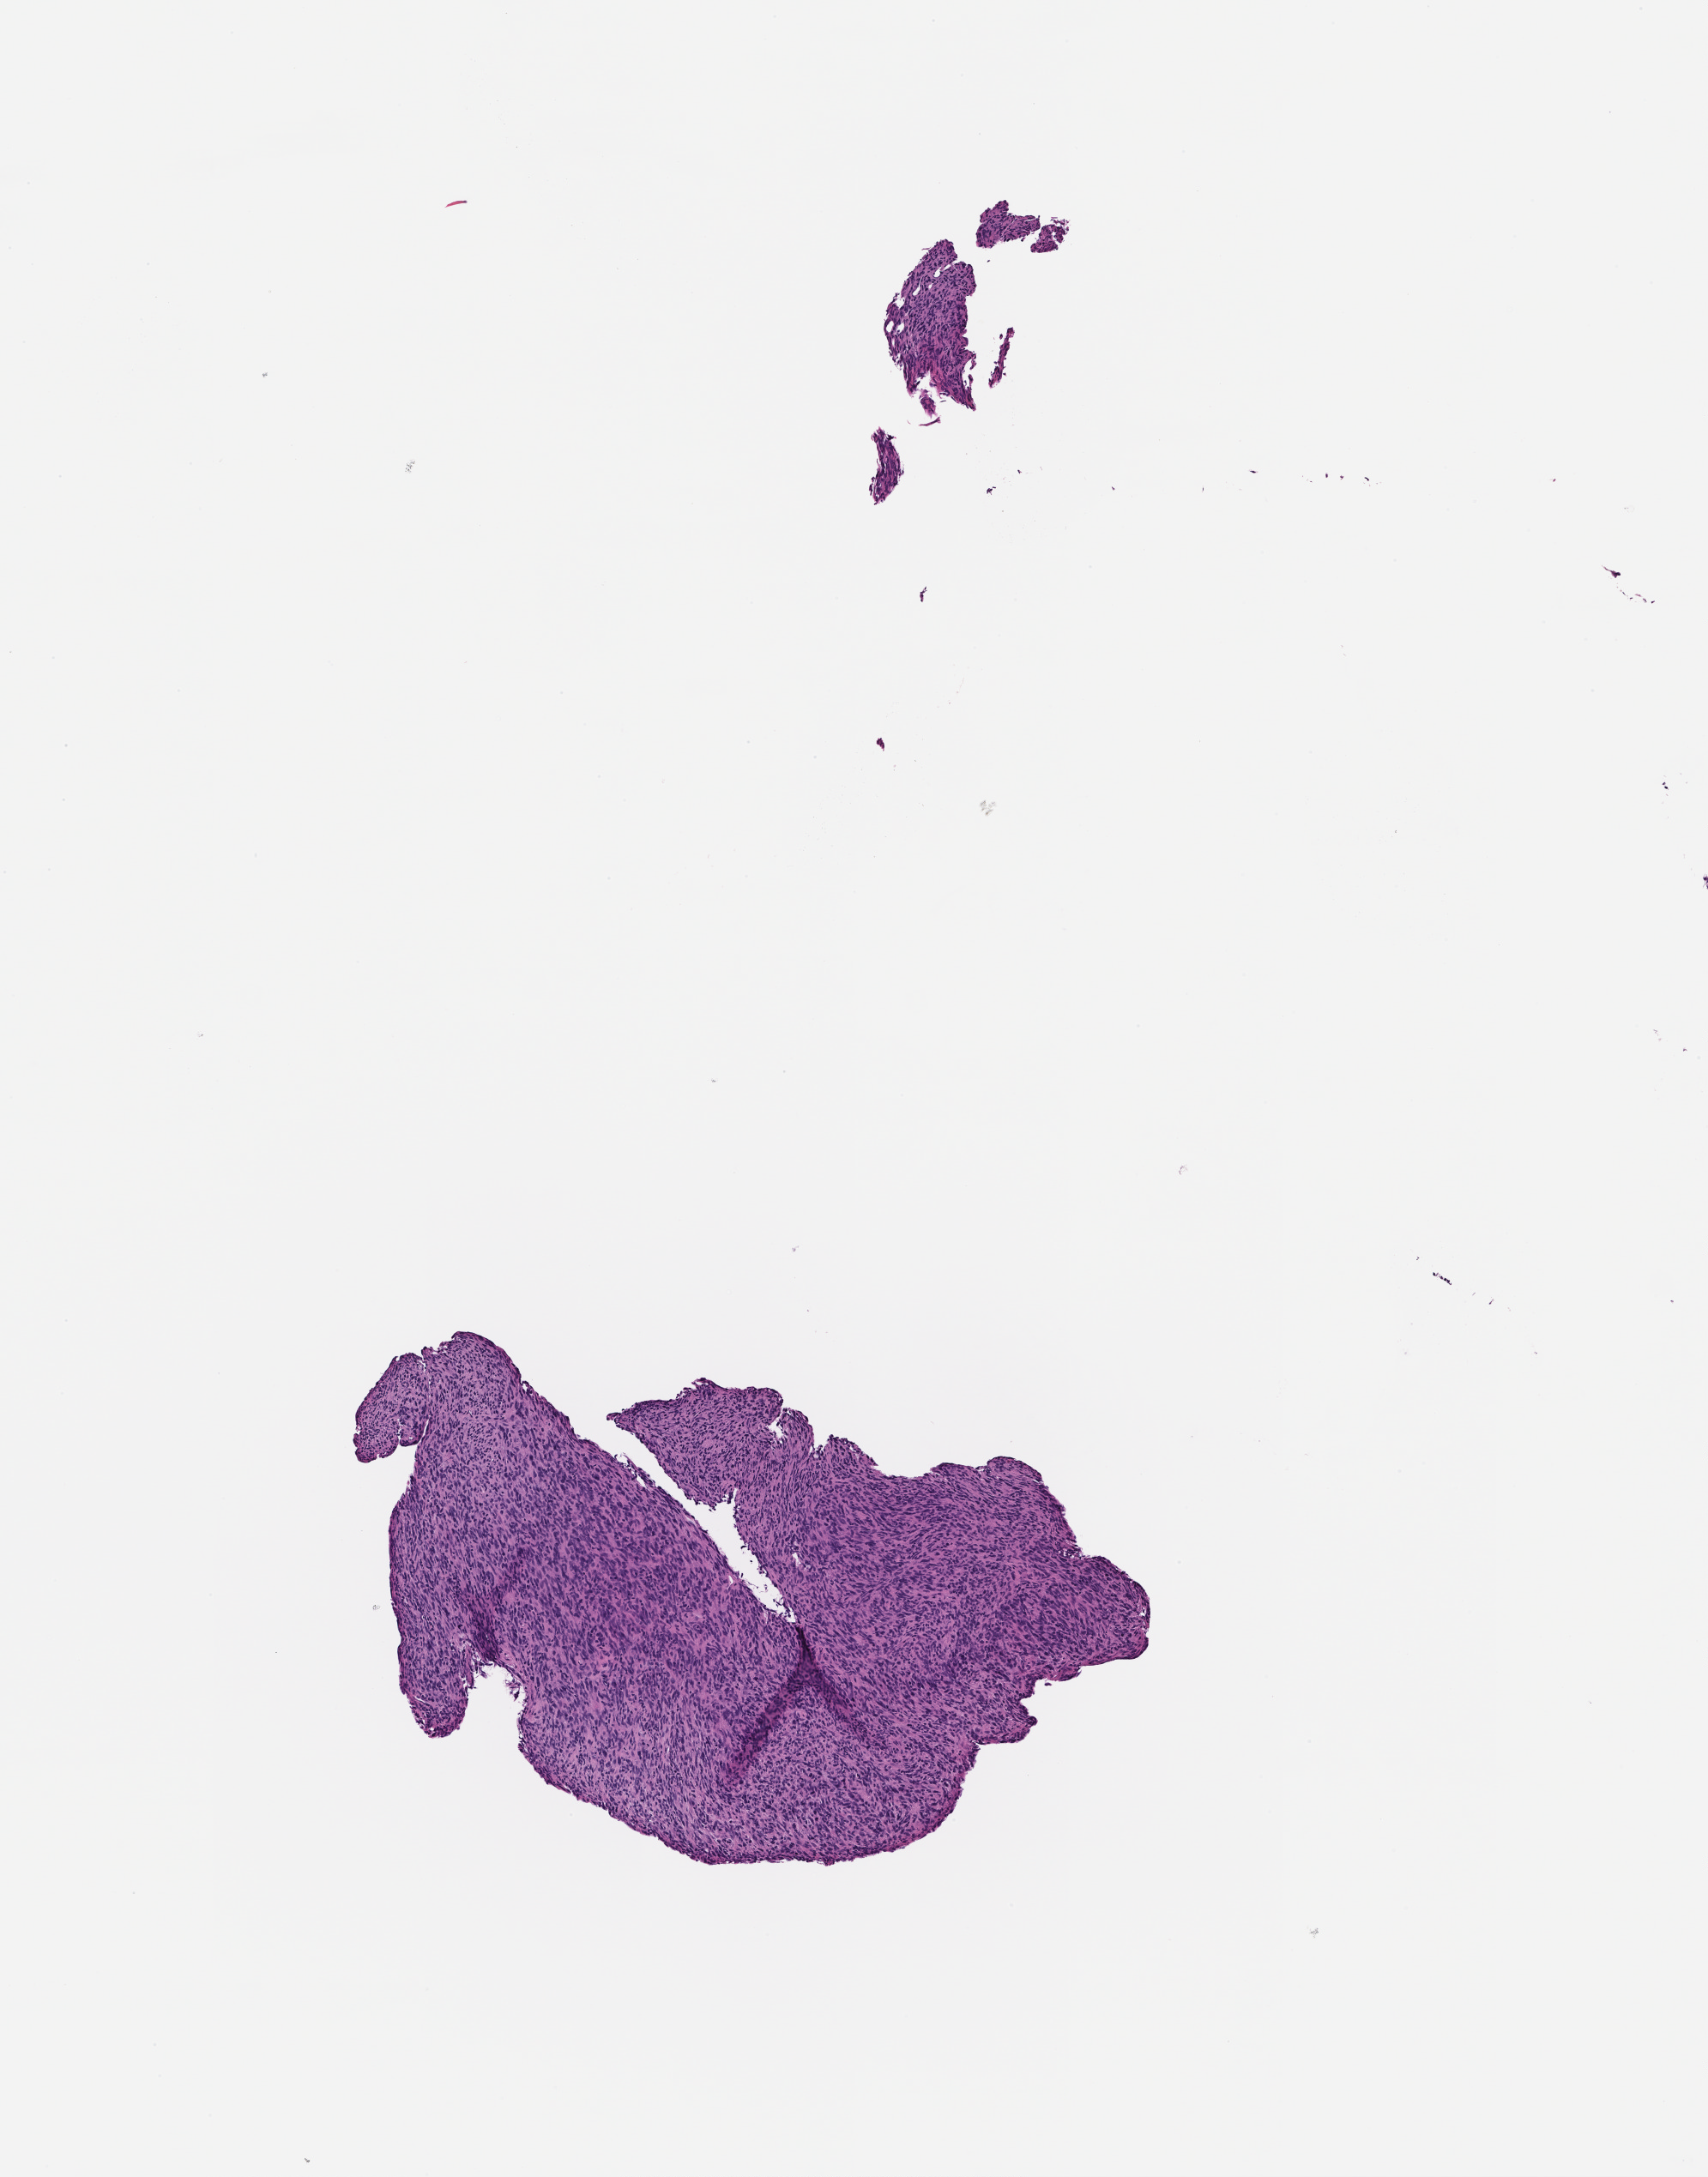
Hematoxylin and eosin (H&E) whole-slide image, shown as a low-resolution overview of the whole scanned area (about 4.0 x 5.1 mm); formalin-fixed paraffin-embedded section. Patient sex: female.
This section: metastatic tumor tissue. Primary diagnosis of the patient: Small Cell Lung Carcinoma.